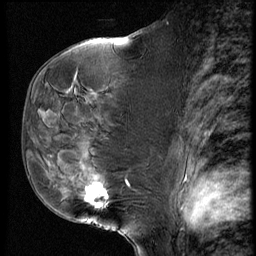
Breast MRI (dynamic contrast-enhanced), one sagittal slice; position 32 of 60 along the scan axis; dynamic contrast-enhanced series, image 2 of 4 at this slice position (ordered by acquisition); 1.5 T; TE 4.2 ms, TR 9 ms; 2.5 mm slice thickness; 256 × 256 image matrix, field of view 180 × 180 mm. Patient: female, 50 years. From the clinical record (not read from this slice): setting: breast cancer imaged before/during neoadjuvant chemotherapy; receptor status: HR-positive, HER2-negative.
Outlined on this slice (semi-automatically segmented with operator editing):
- analysis volume of interest (the breast-tissue region the enhancement analysis was run in; not a lesion): bounding box [x1, y1, x2, y2] px = [48, 109, 135, 230]
- tumour enhancement mask (voxels above the 140 % enhancement threshold inside the analysis volume of interest): [84, 186, 108, 208]